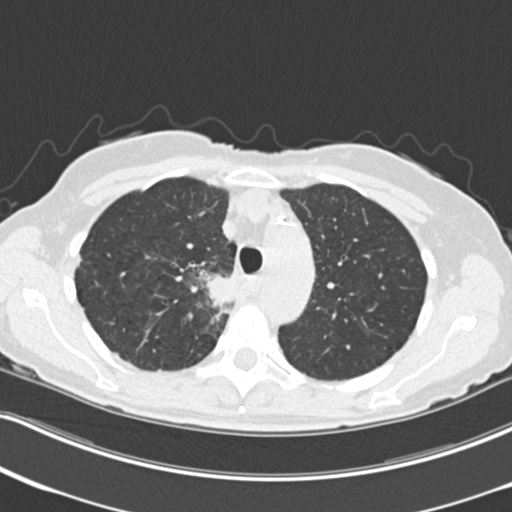
Low-dose screening chest CT, one axial slice. Slice 170 of 226 in the series (ordered by position). Reconstruction kernel B30f. 120 kVp. Lung window (W 1500 / L -600 HU). 2 mm slice thickness. 512 × 512 image matrix.
Annotated regions visible in this slice (outlined manually by an expert reader):
- lesion 1 (tumor, mediastinum): bounding box [x1, y1, x2, y2] px = [206, 276, 234, 309]